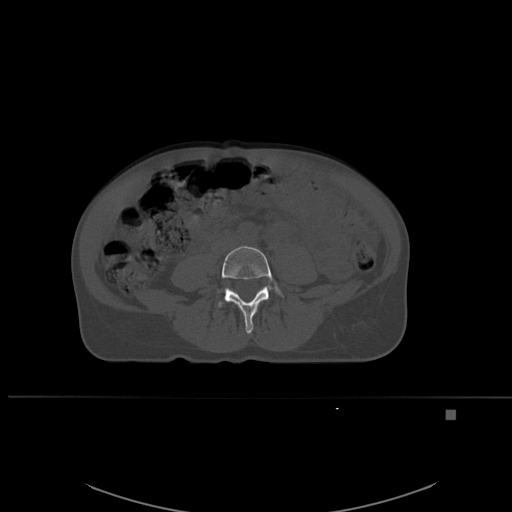
CT including the spine, one axial slice. Slice 190 of 537 in the series (ordered by position). Bone window (W 1800 / L 400 HU). 1.5 mm slice thickness. 512 × 512 image matrix, field of view 440 × 440 mm. Female patient, age 45 years. Case-level facts recorded for this patient, not image findings: primary cancer: lung.
Annotated regions visible in this slice (semi-automatically segmented with operator editing):
- L4 vertebra: bounding box <217,245,284,334> (left, top, right, bottom; pixels)